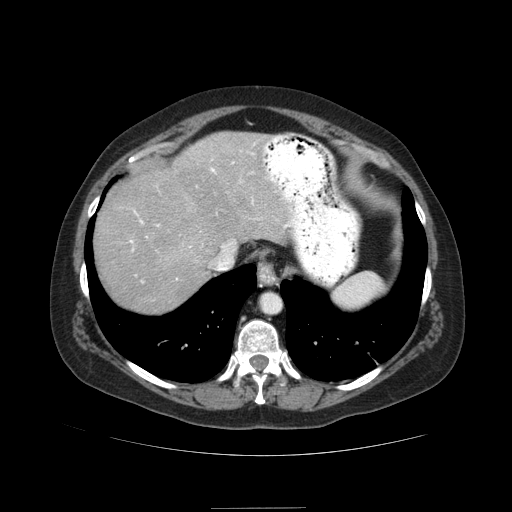
Contrast-enhanced abdominal CT (liver protocol), one axial slice; reconstruction kernel STANDARD; soft-tissue window (W 400 / L 40 HU); 512 × 512 image matrix. From the clinical record (not read from this slice): diagnosis: hepatocellular carcinoma (patient treated with transarterial chemoembolisation; whether this scan precedes or follows treatment is not stated here); TNM stage (as recorded): Stage-IIIB; Child-Pugh class: A.
Annotated regions visible in this slice (semi-automatically segmented with operator editing):
- liver parenchyma outside the tumour (the mass and vessels are separate outlines, so this box may not span the whole liver): box from (x=94, y=132) to (x=293, y=314) px
- liver vessels: (x=130, y=168)–(x=293, y=251)